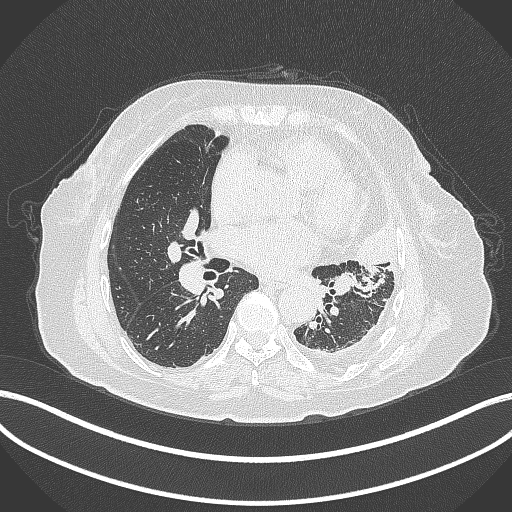
Chest CT, one axial slice; slice 176 of 399 in the series (ordered by position); reconstruction kernel B70f; 120 kVp; lung window (W 1500 / L -600 HU); 1 mm slice thickness; 512 × 512 image matrix. Patient: female, 75 years. From the clinical record (not read from this slice): clinical TNM (as recorded): T3 N3 M1.
Annotated regions visible in this slice (bounding box drawn by a radiologist):
- lung tumour (recorded histology: adenocarcinoma): bounding box <354,218,403,271> (left, top, right, bottom; pixels)